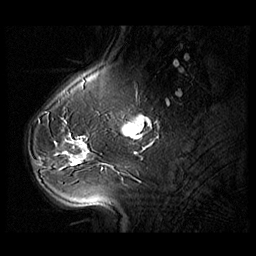
Breast MRI (dynamic contrast-enhanced), one sagittal slice; position 29 of 104 along the scan axis; 3 images stored at this slice position (order not interpretable as contrast timing); 1.5 T; TE 1.3 ms, TR 5.5 ms; 3 mm slice thickness; 256 × 256 image matrix. Female patient, age 54 years. From the clinical record (not read from this slice): setting: breast cancer imaged before/during neoadjuvant chemotherapy; receptor status: HR-positive, HER2-negative.
Outlined on this slice (semi-automatically segmented with operator editing):
- analysis volume of interest (the breast-tissue region the enhancement analysis was run in; not a lesion): bounding box (x1, y1, x2, y2) in pixels: (28, 127, 104, 182)
- tumour enhancement mask (voxels above the 140 % enhancement threshold inside the analysis volume of interest): (43, 136, 89, 165)